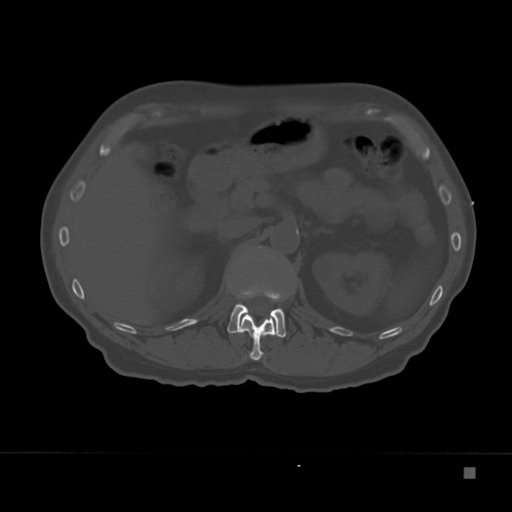
CT including the spine, one axial slice; position 120 of 332 along the scan axis; reconstruction kernel Br40s; 120 kVp; bone window (W 1800 / L 400 HU); 512 × 512 image matrix. Patient: male, 72 years. Case-level facts recorded for this patient, not image findings: primary cancer: skeletal.
Annotated regions visible in this slice (semi-automatic segmentation, software-assisted and operator-edited):
- L1 vertebra: box from (x=227, y=247) to (x=286, y=338) px
- T12 vertebra: (x=241, y=290)–(x=275, y=361)